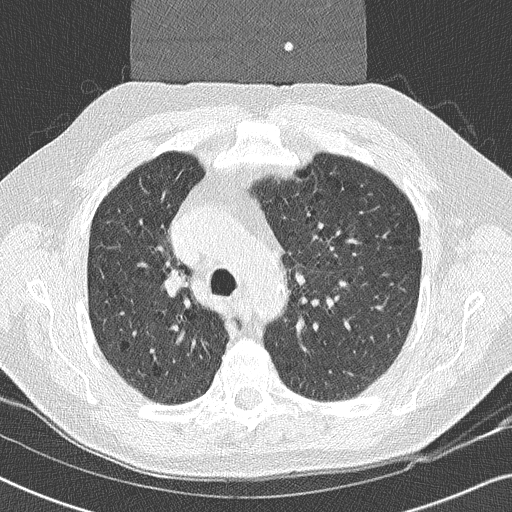
Low-dose screening chest CT, one axial slice; position 172 of 252 along the scan axis; 120 kVp; lung window (W 1500 / L -600 HU); 2 mm slice thickness; 512 × 512 image matrix, field of view 330 × 330 mm.
Annotated regions visible in this slice (manually delineated by an expert):
- lesion 1 (tumor, upper lobe of right lung): bounding box (x1, y1, x2, y2) in pixels: (164, 271, 185, 295)